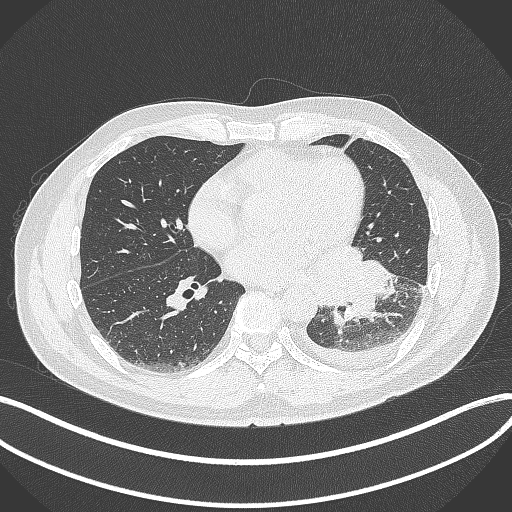
Chest CT, one axial slice; position 153 of 342 along the scan axis; reconstruction kernel B70f; 120 kVp; lung window (W 1500 / L -600 HU); 1 mm slice thickness; 512 × 512 image matrix. Male patient, age 58 years. From the clinical record (not read from this slice): clinical TNM (as recorded): T3 N1 M1b.
Annotated regions visible in this slice (rectangle marked by the reading radiologist):
- lung tumour (recorded histology: small cell carcinoma): bounding box (x1, y1, x2, y2) in pixels: (315, 245, 398, 330)